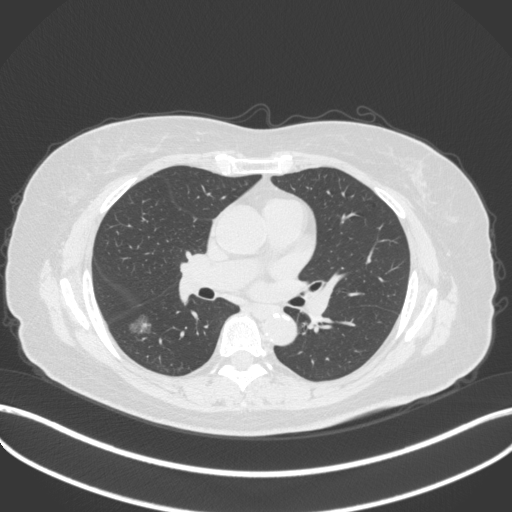
Chest CT, one axial slice. Slice 173 of 322 in the series (ordered by position). Reconstruction kernel B31f. Lung window (W 1500 / L -600 HU). 512 × 512 image matrix, field of view 400 × 400 mm. Female patient, age 64 years. Case-level facts recorded for this patient, not image findings: clinical TNM (as recorded): T1c N0 M0; histopathological grade: G1.
Outlined on this slice (bounding box drawn by a radiologist):
- lung tumour (recorded histology: adenocarcinoma): bounding box [x1, y1, x2, y2] px = [126, 312, 151, 339]